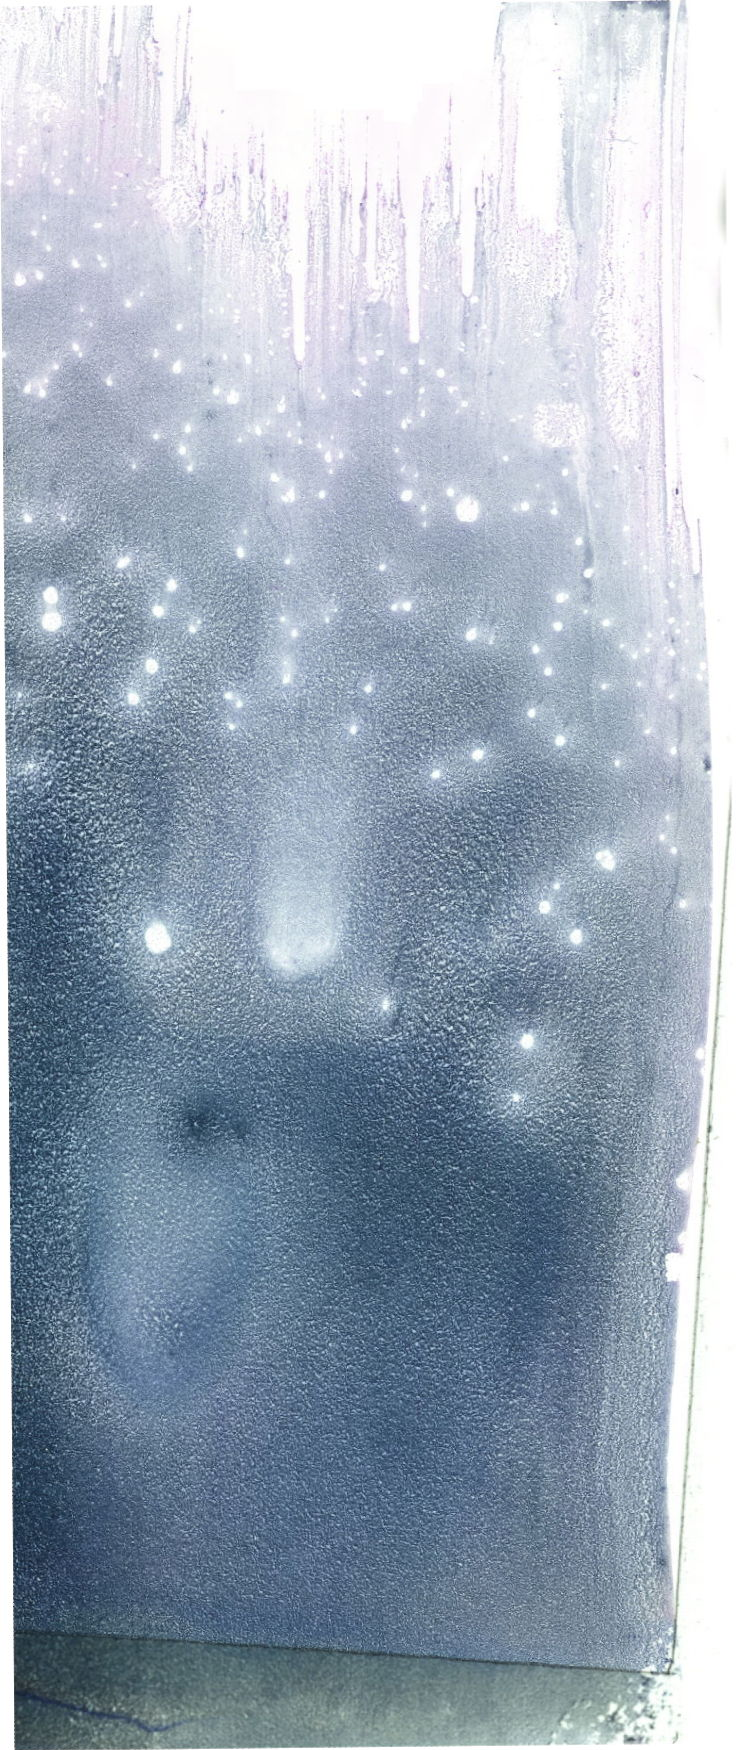
May-Grünwald-Giemsa (MGG)-stained marrow aspirate smear (whole slide), whole scanned area (about 20.9 x 49.6 mm) shown as a low-resolution overview. Female patient.
• diagnosis: B Acute Lymphoblastic Leukemia